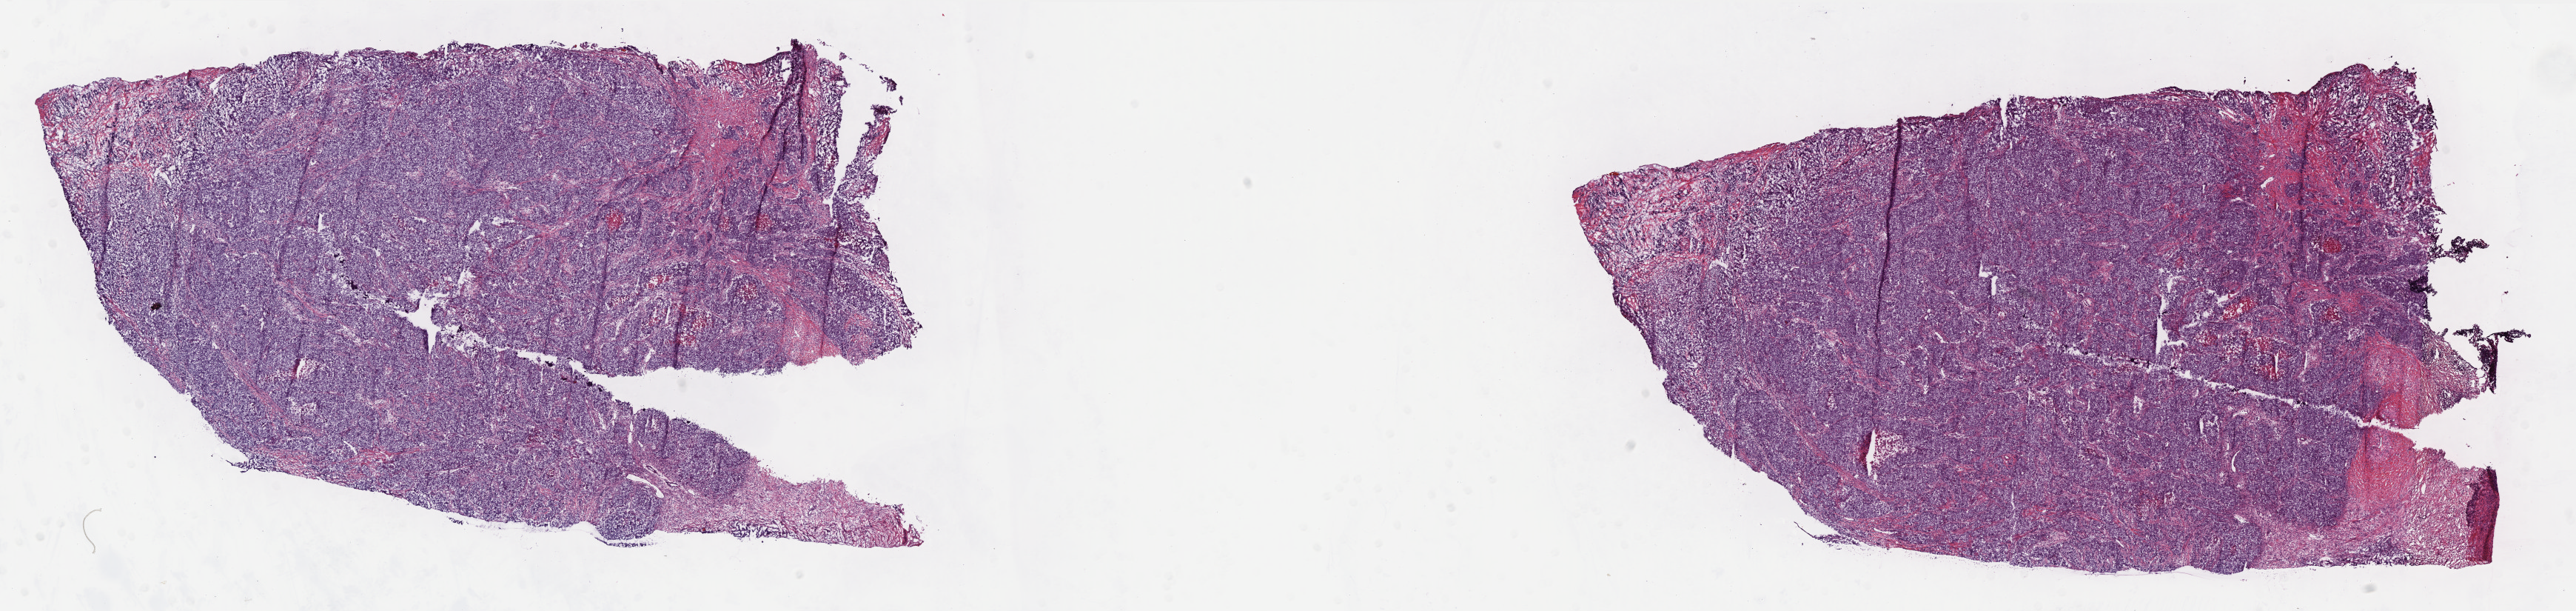
Digitized H&E-stained tissue section (whole slide), whole scanned area (about 27.9 x 6.6 mm) shown as a low-resolution overview, frozen section, breast, primary tumour sample. Female patient; age at initial diagnosis 56 years. Pathologist review of this section (percent, as recorded): tumour cells 80%, tumour nuclei 85%.
Pathologic diagnosis: Infiltrating duct carcinoma, NOS.